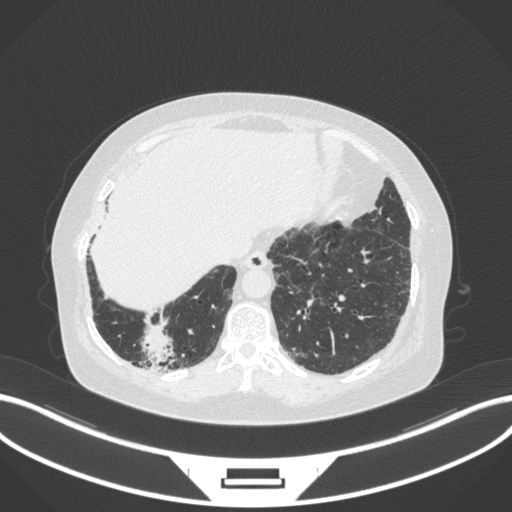
Chest CT, one axial slice. Slice 29 of 303 in the series (ordered by position). 120 kVp. Lung window (W 1500 / L -600 HU). 1 mm slice thickness. 512 × 512 image matrix, field of view 400 × 400 mm. Patient: female, 65 years. From the clinical record (not read from this slice): clinical TNM (as recorded): T2b N1 M0.
Outlined on this slice (bounding box drawn by a radiologist):
- lung tumour (recorded histology: adenocarcinoma): bounding box <135,324,178,368> (left, top, right, bottom; pixels)